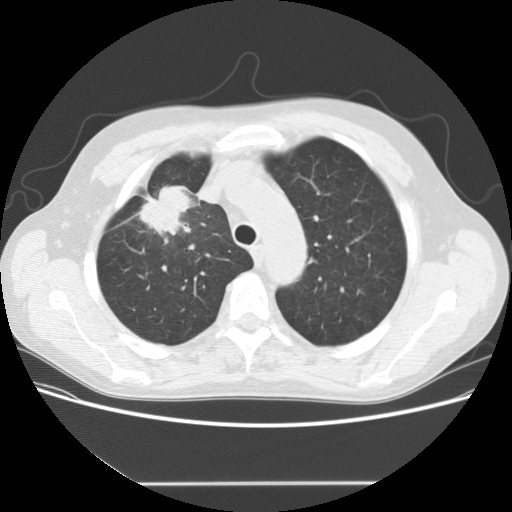
Low-dose screening chest CT, axial slice, baseline screening round, lung window (W 1500 / L -600 HU), standard (soft-tissue) reconstruction kernel (STANDARD), slice 34 of 153 in the series. Male, age 56 years at enrolment.
- Expert-annotated lung lesion, box from (x=128, y=174) to (x=211, y=243) px.
- The screening reader recorded 2 non-calcified nodules or masses ≥4 mm on this exam (right upper lobe, right middle lobe); which of them this box marks is not recorded.
- Lung cancer was diagnosed 120 days after this screen: adenocarcinoma, NOS, right upper lobe, stage IIIA (AJCC 6th edition), 34 mm at pathology.